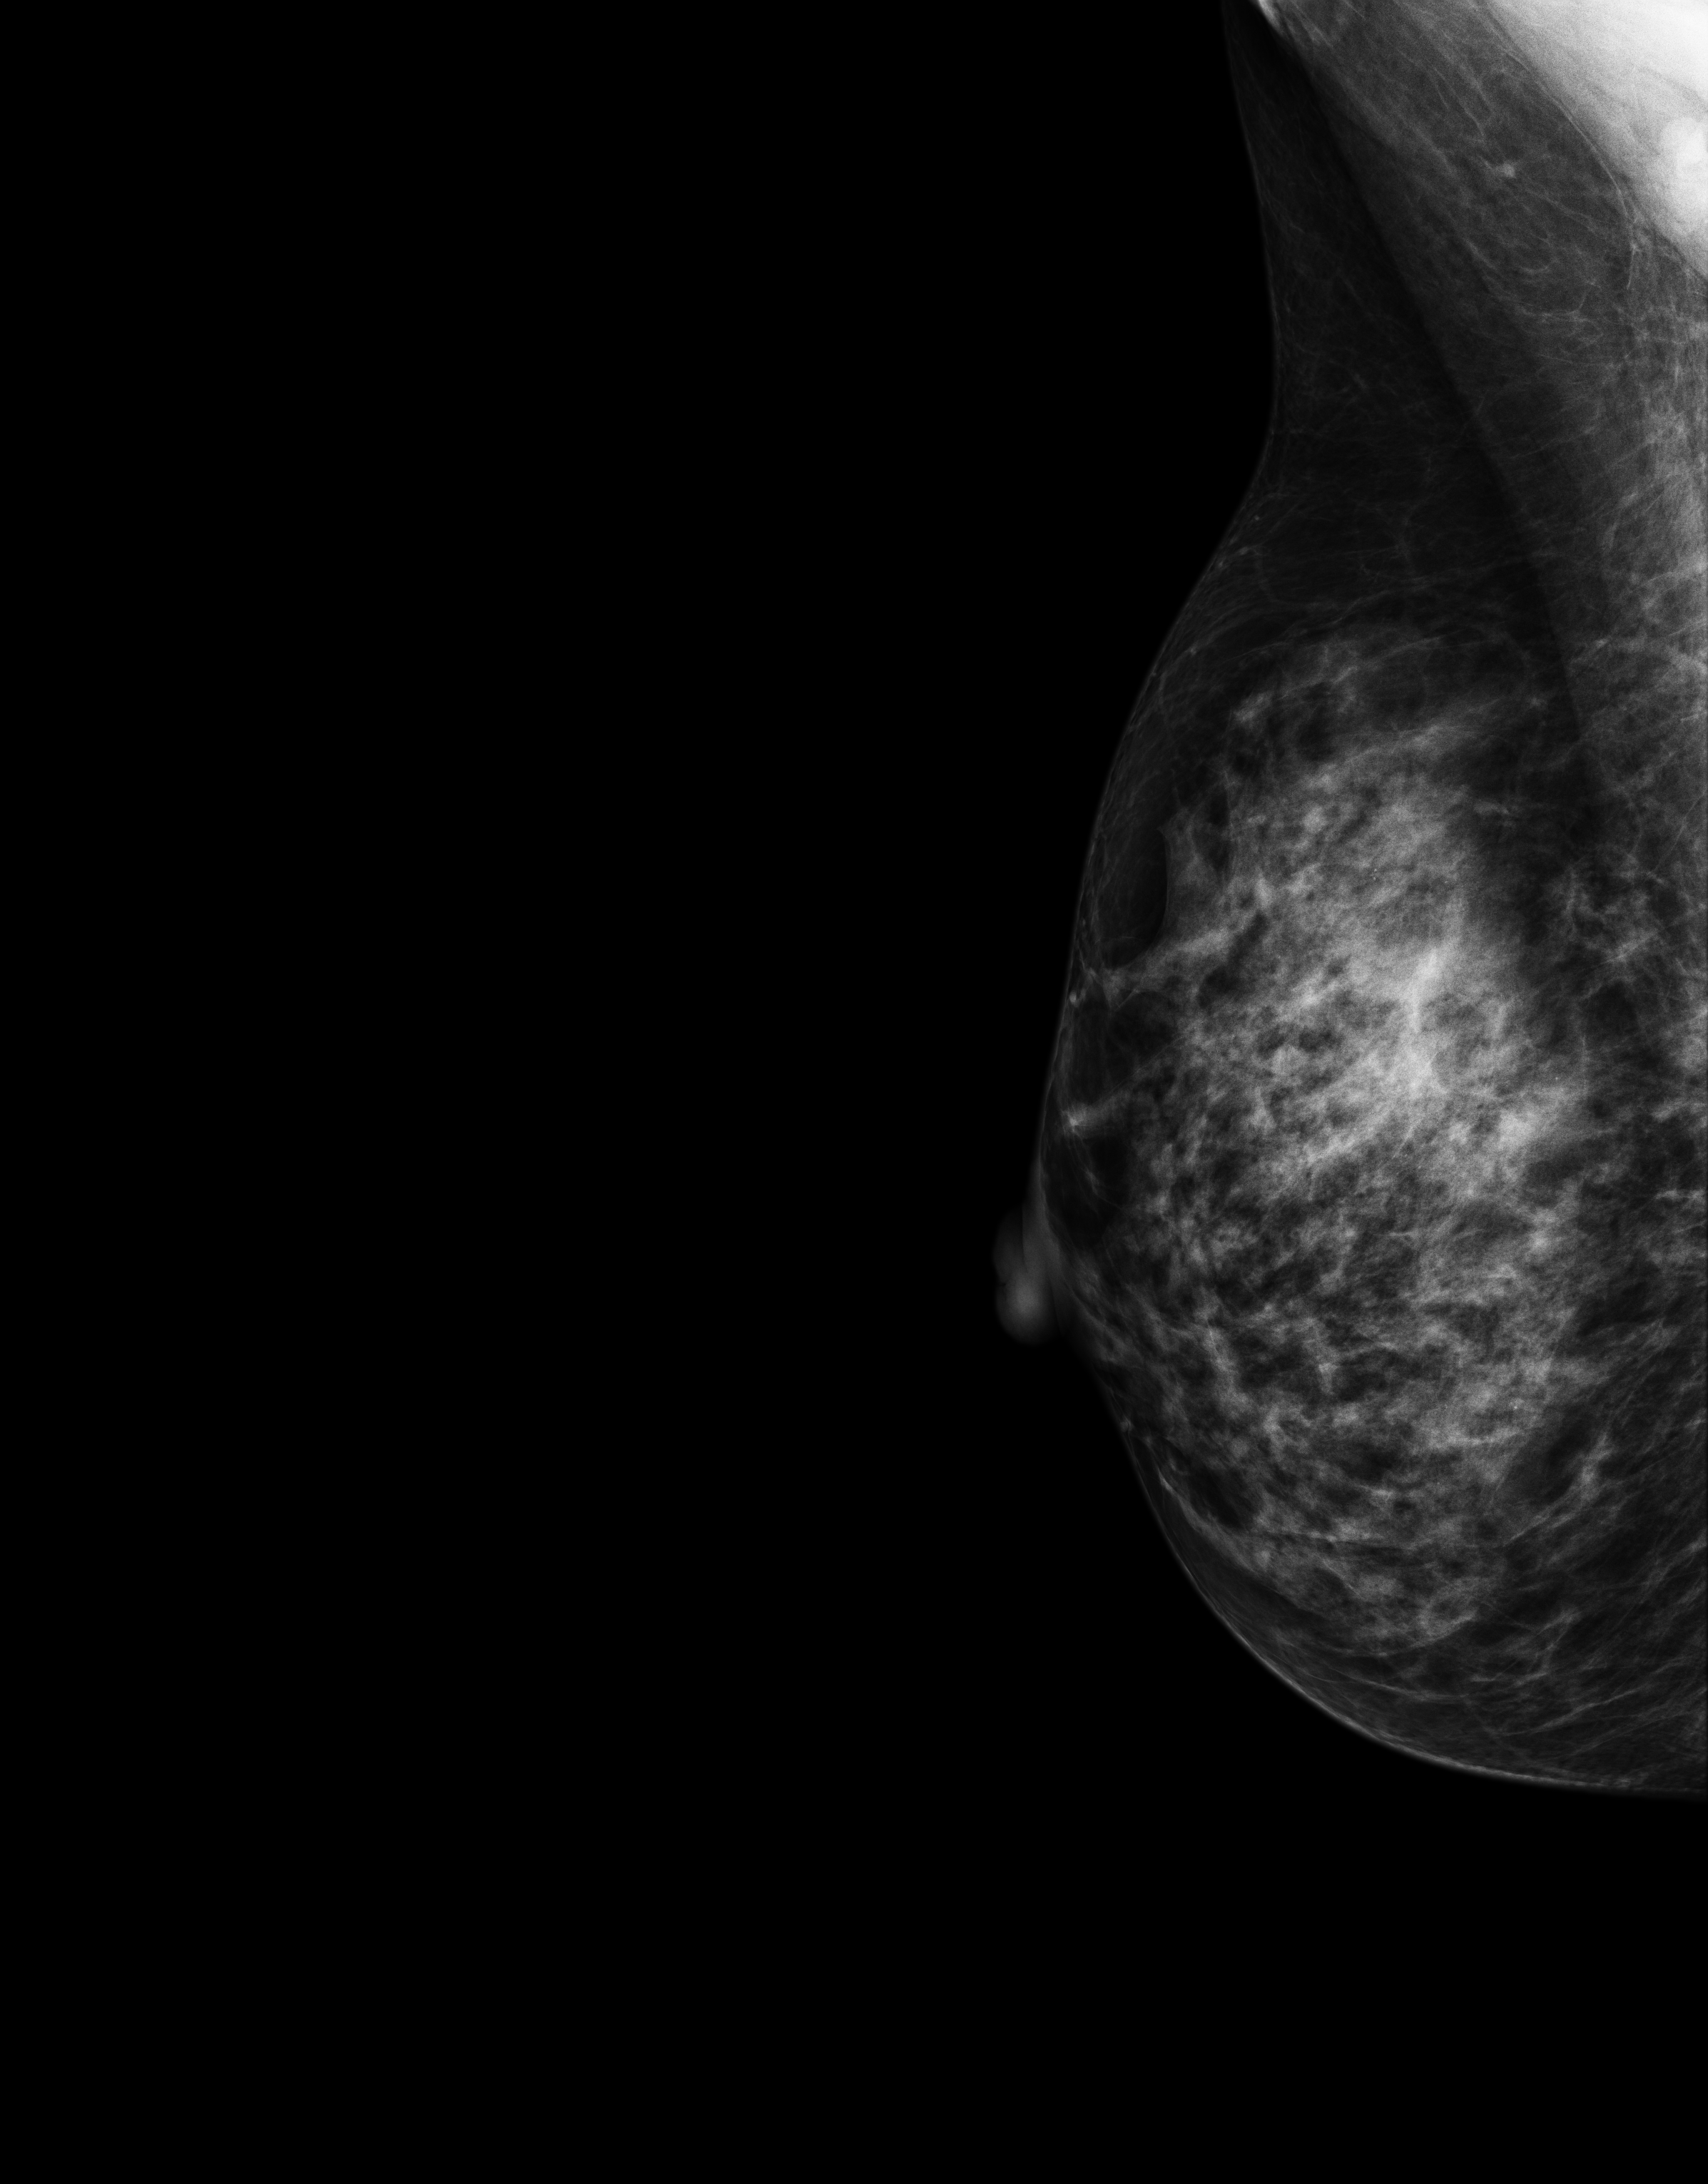
Screening examination; compressed breast thickness 65 mm; system: Senographe Essential ADS_56.21.3. Patient aged 43 years (female).
Image type: full-field digital mammogram. Breast: right. Projection: mediolateral oblique (MLO) view.